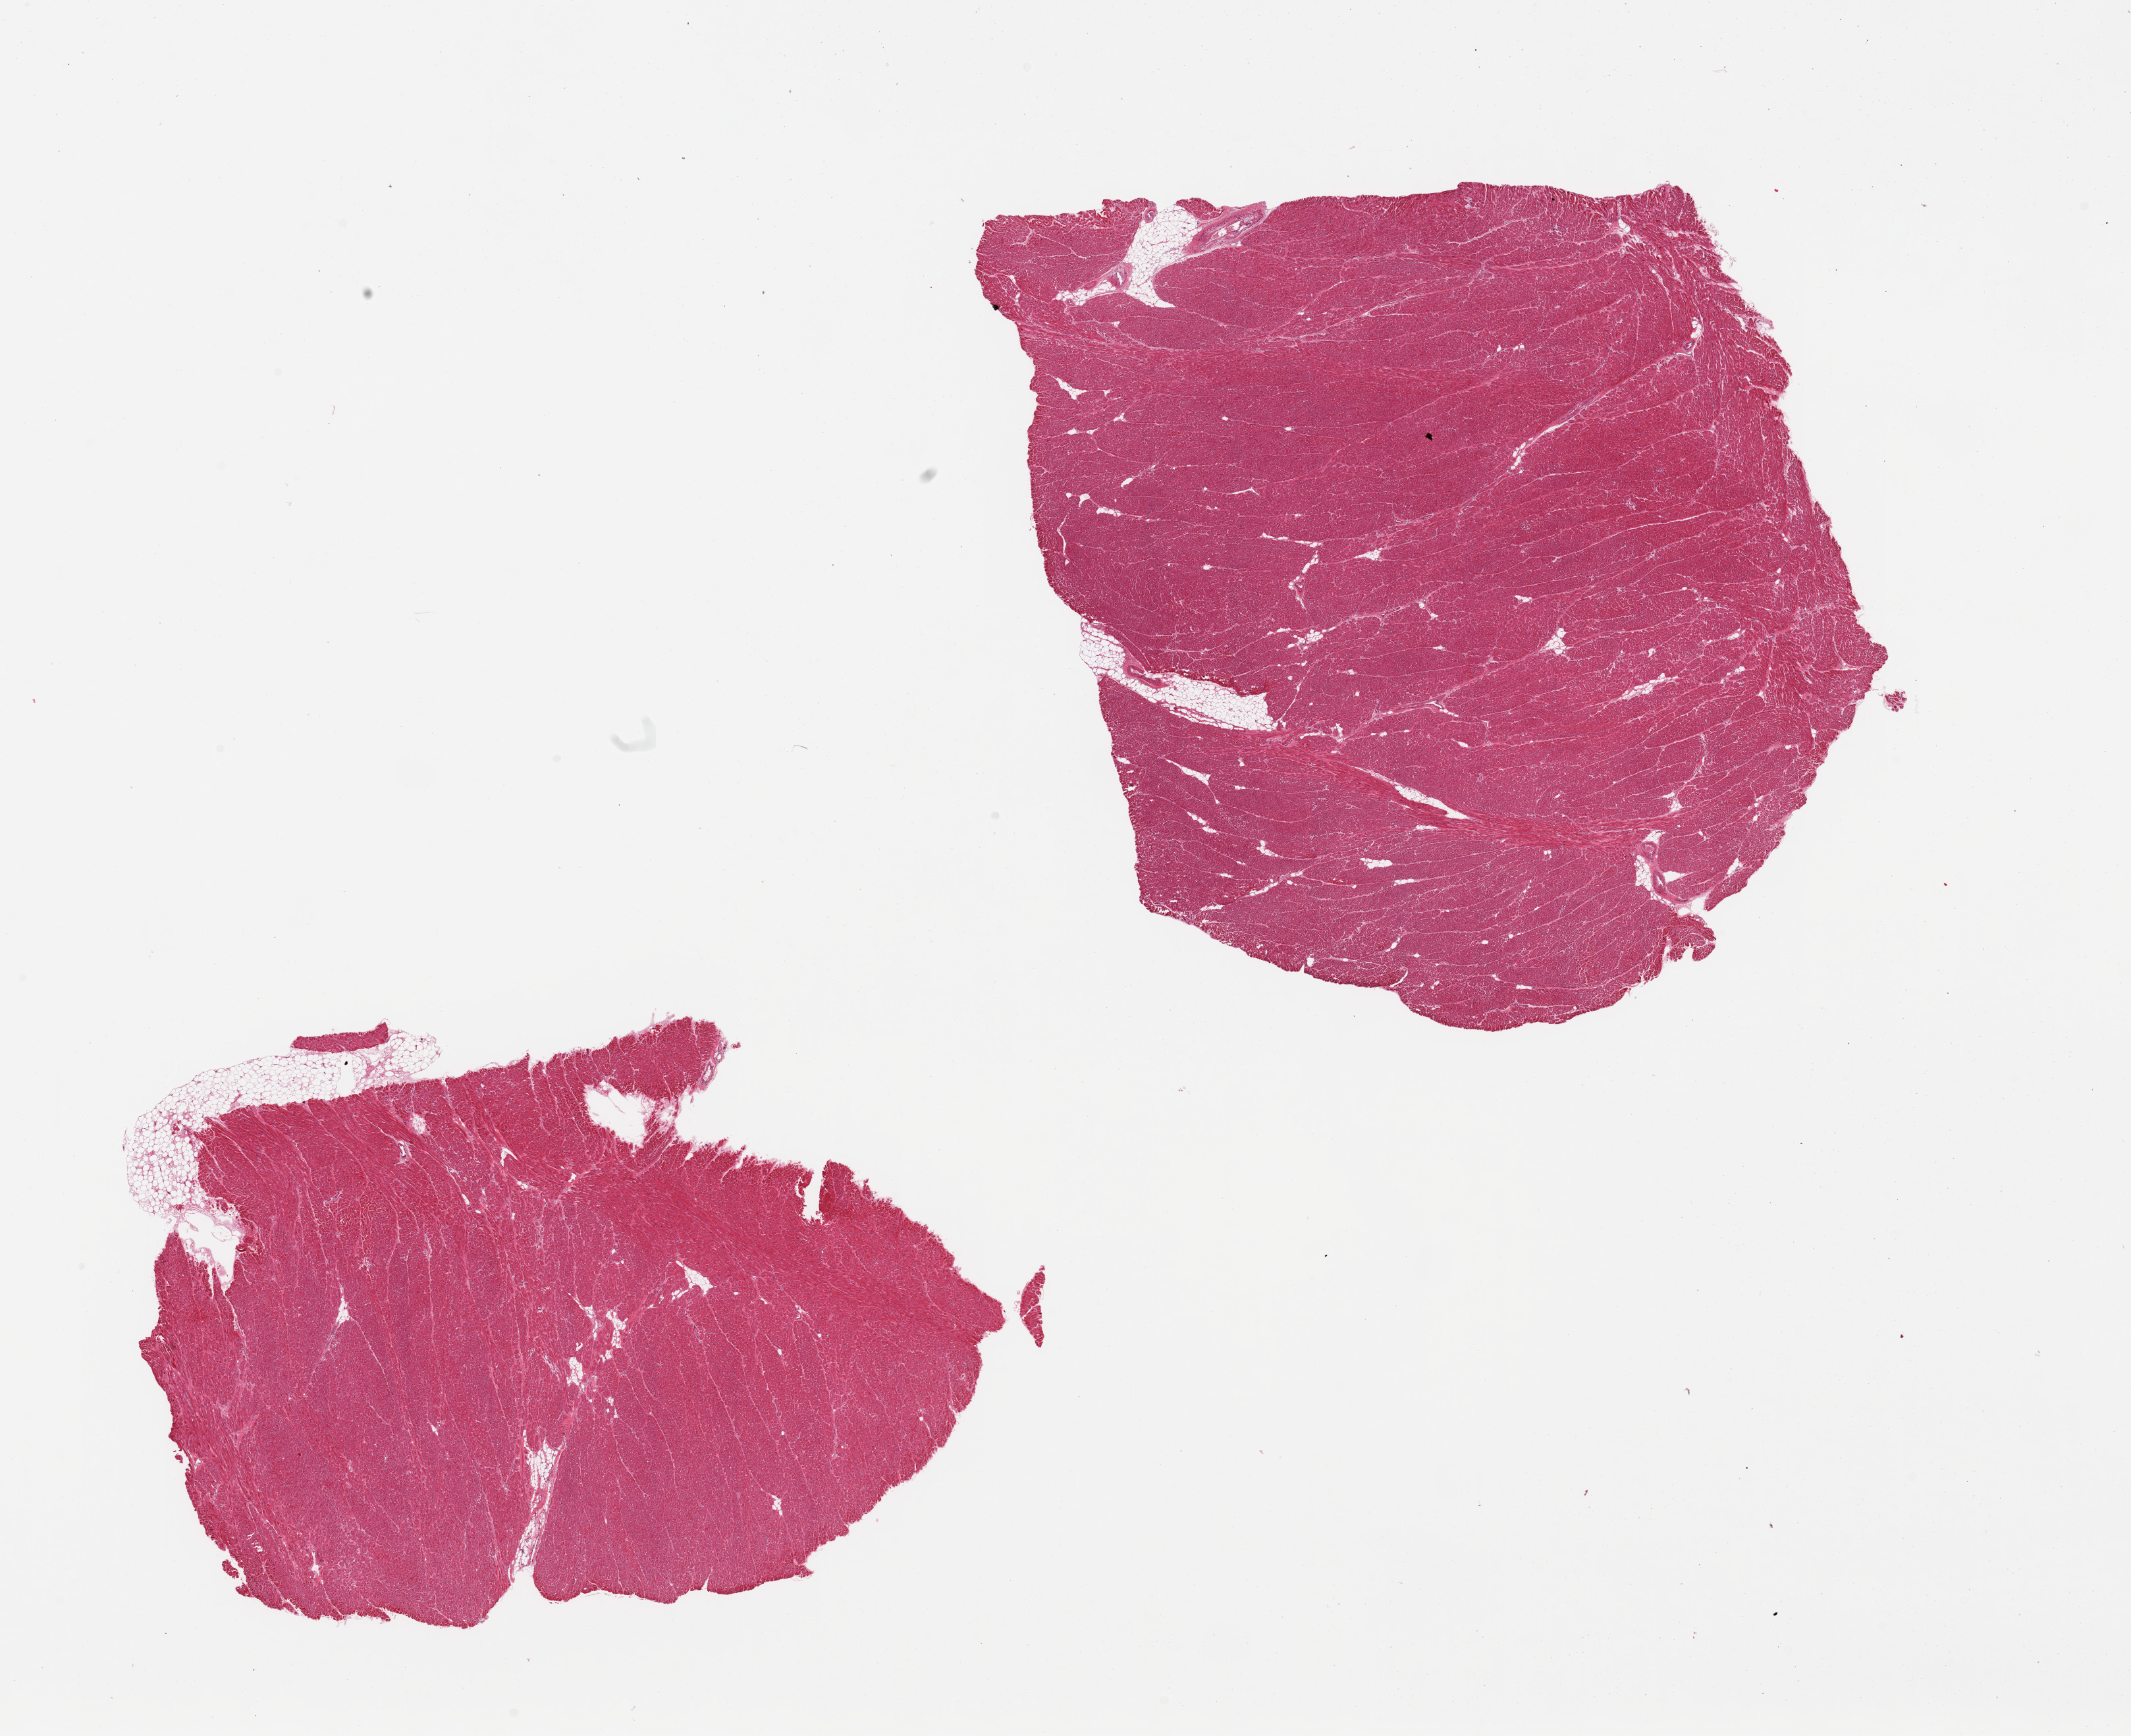
Digitized H&E-stained section, shown as a low-resolution overview of the whole scanned area (about 25.6 x 20.8 mm). PAXgene-fixed paraffin-embedded (PFPE) section. Sampled site (target tissue): heart. Tissue donor sample. Female donor.
Pathologist's review note for this sample: 2 pieces; 5% fat; hypertrophied muscle.